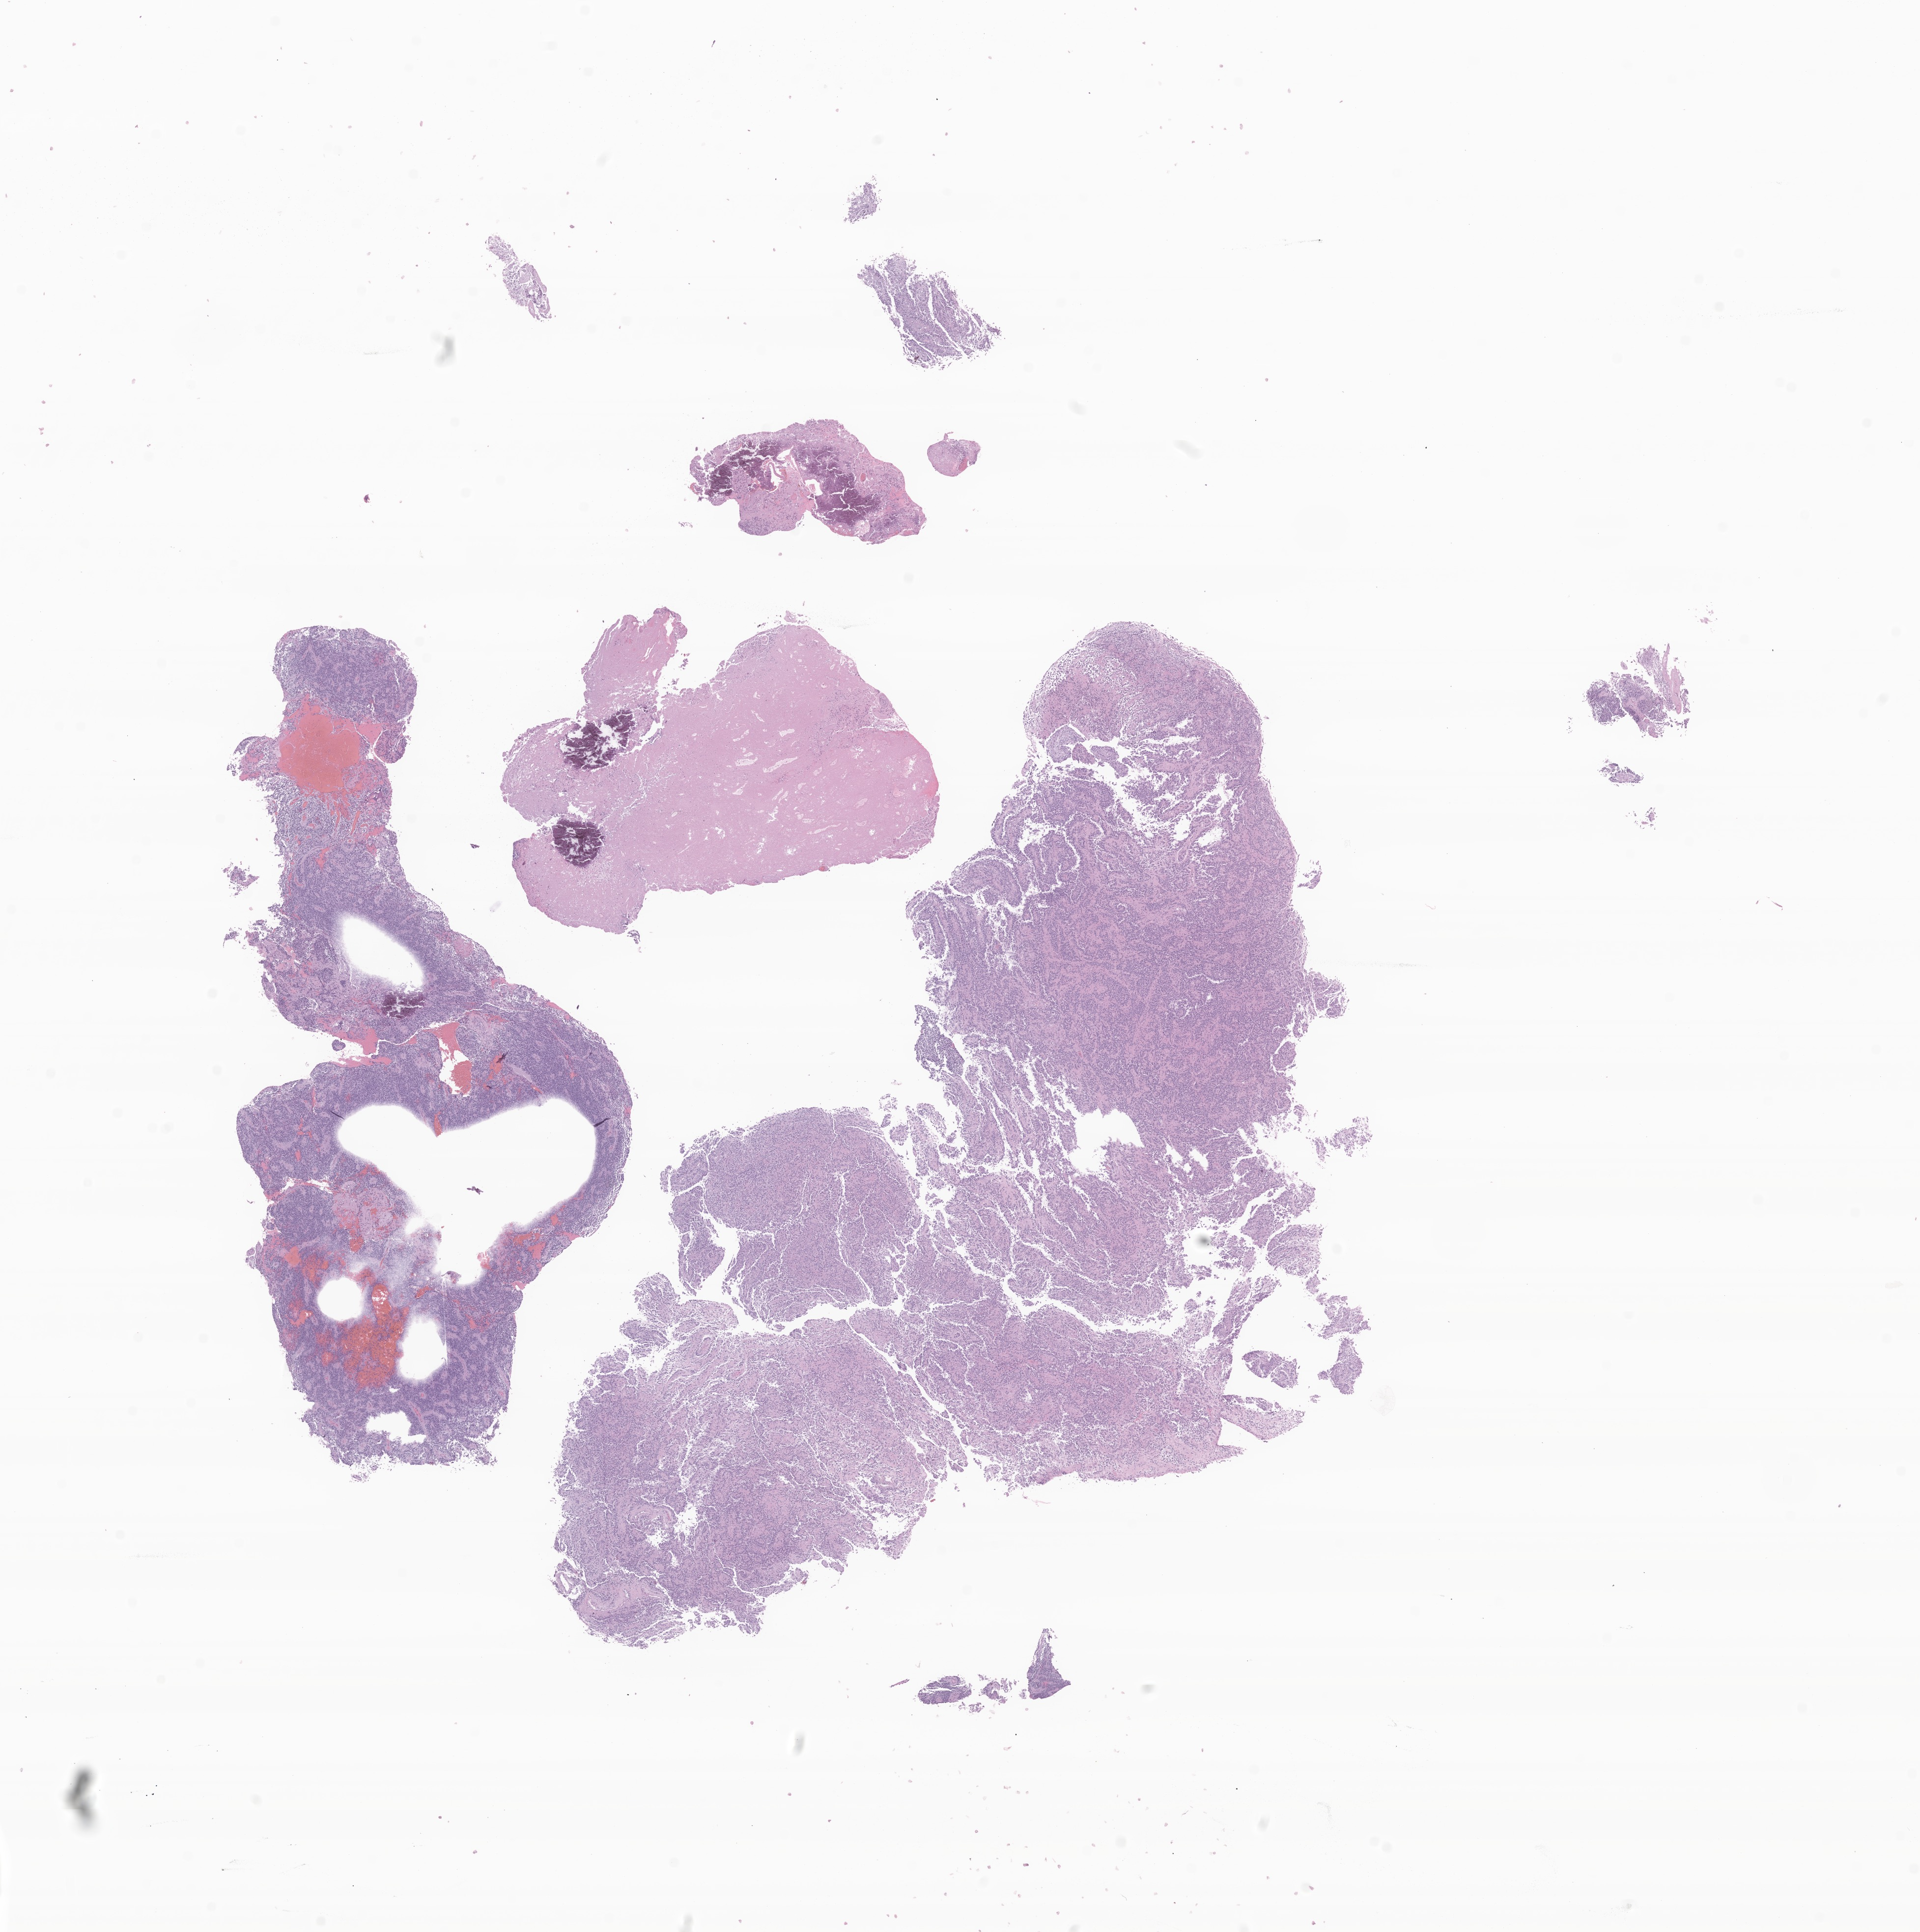
Hematoxylin and eosin (H&E) whole-slide image of tumor tissue from the brain, low-resolution overview of the scanned area, about 16.5 x 16.6 mm, FFPE section. Patient: female, age 774 days (about 2.1 years).
Recorded diagnosis: Ependymoma, anaplastic.